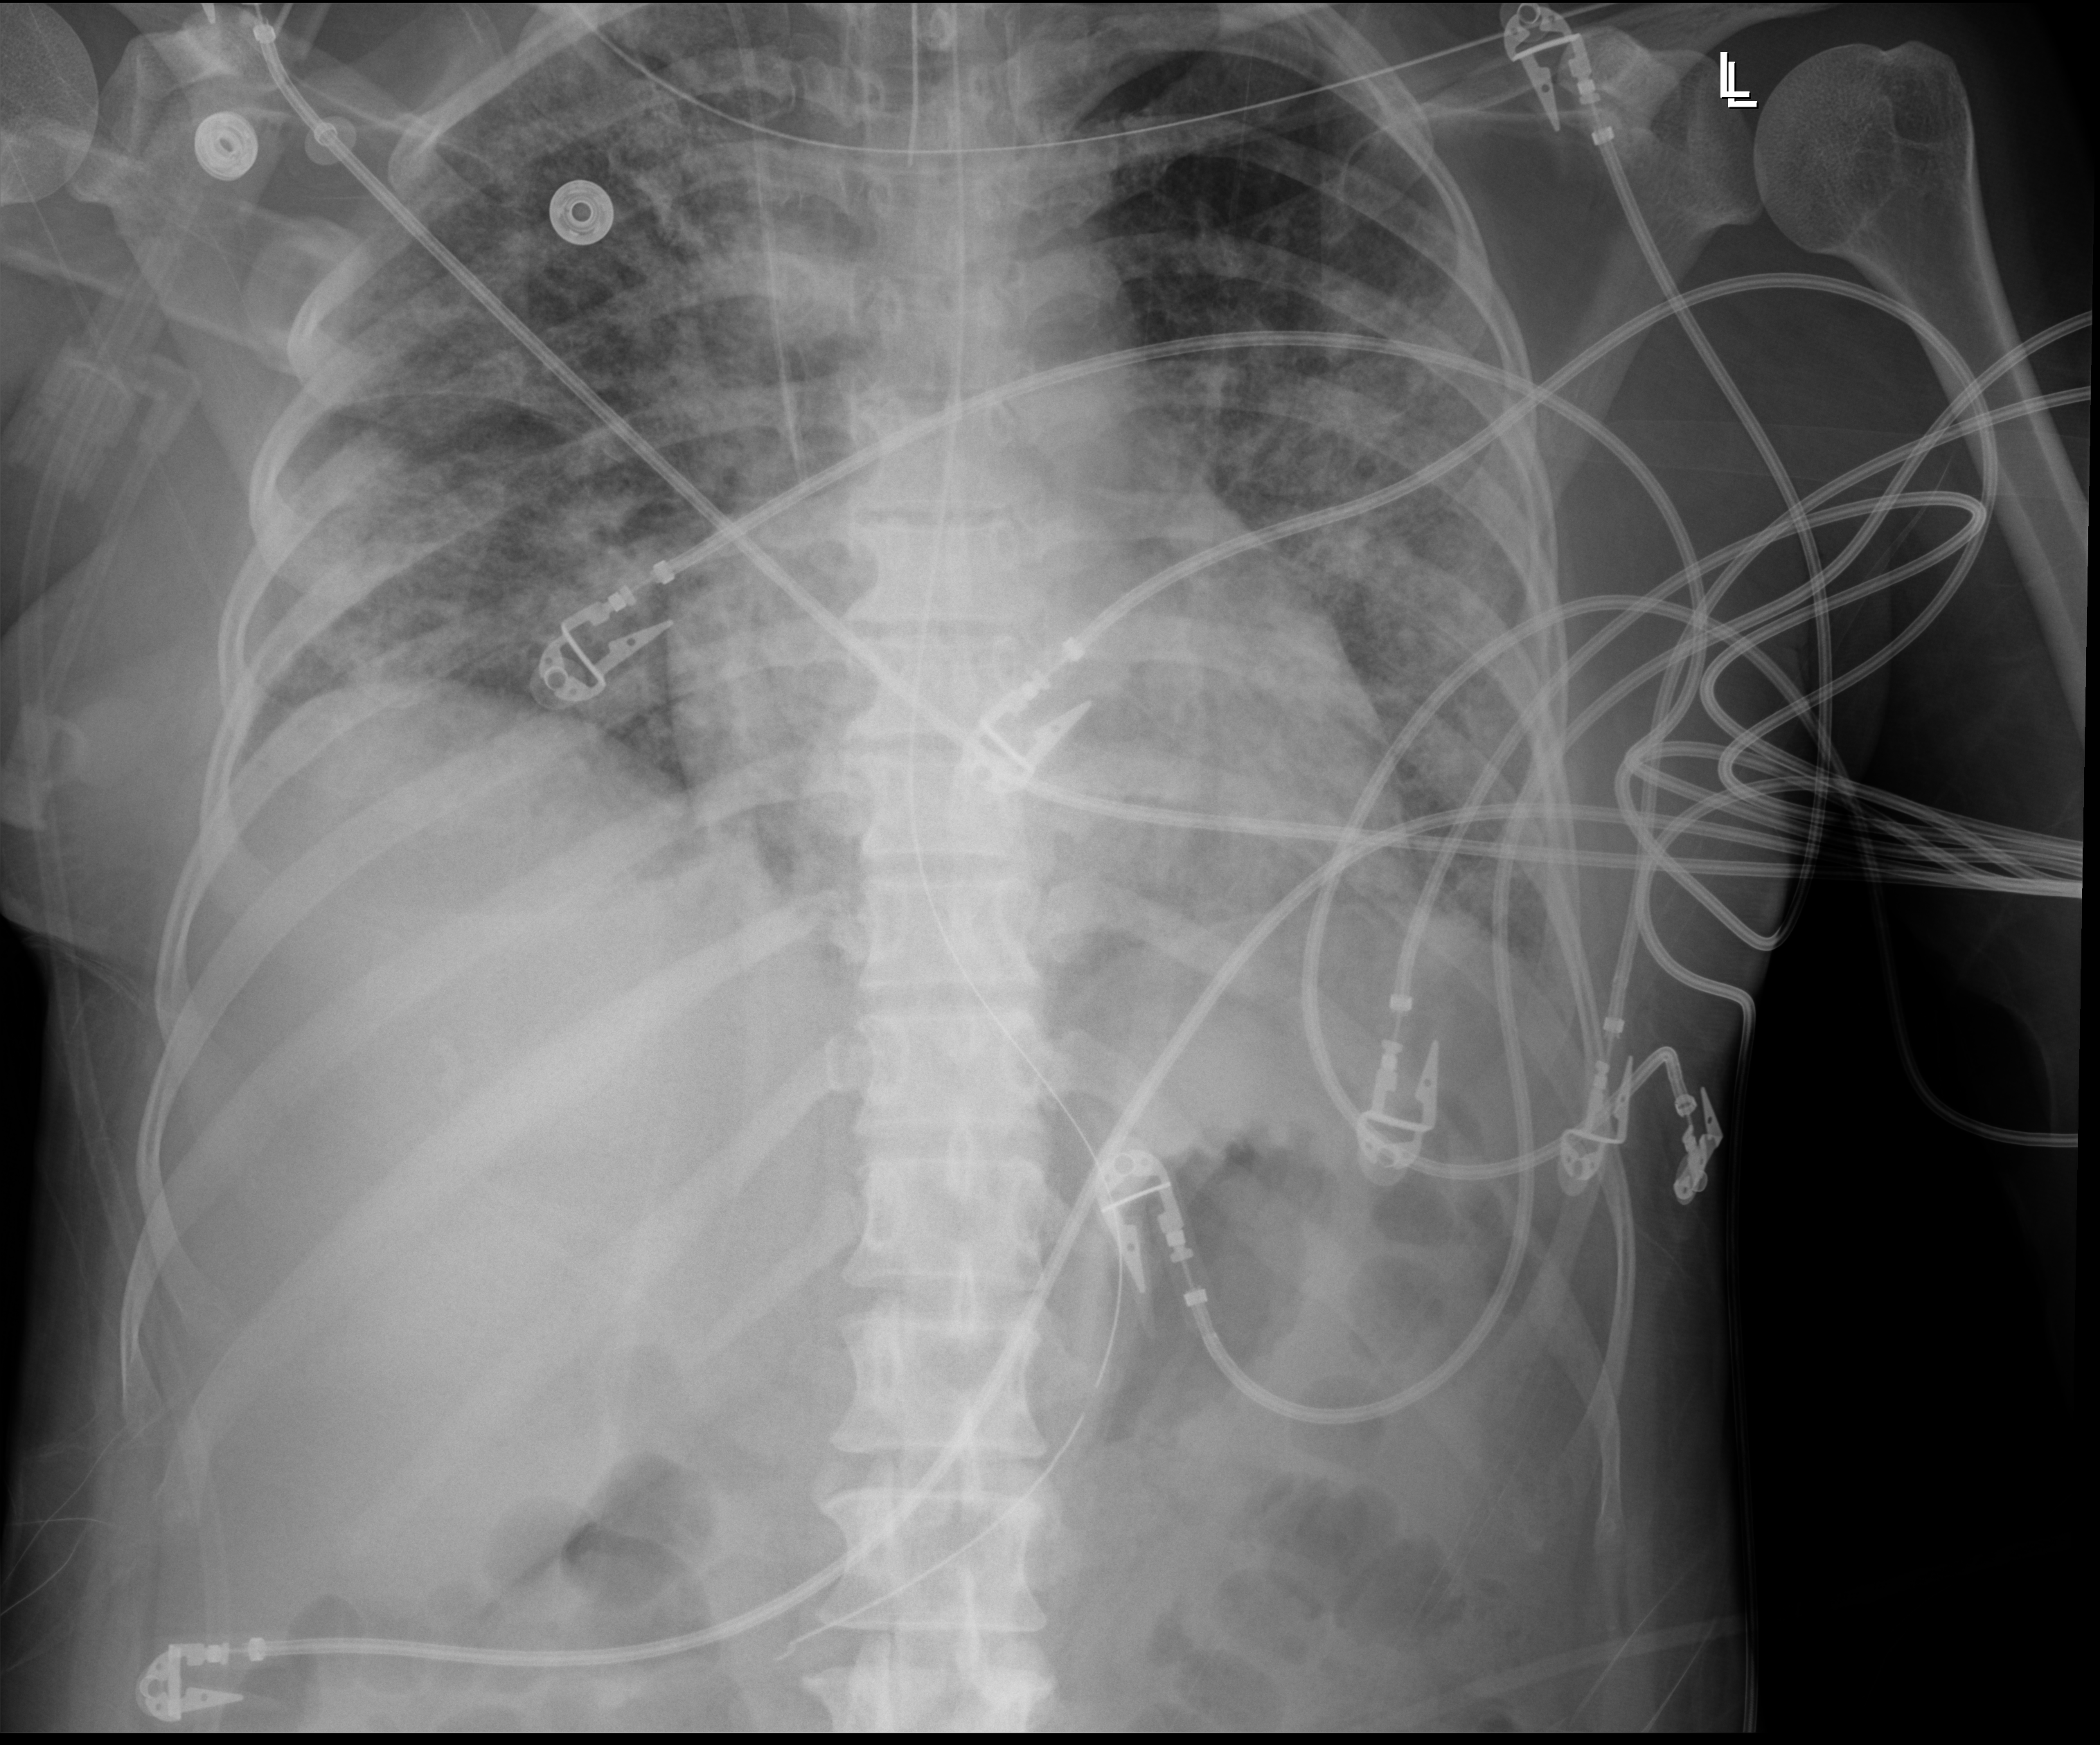
Portable chest radiograph. Female patient hospitalised with COVID-19, age 18–59 years.
Hospital-stay facts (about this admission, not read from this image; timing relative to this image not recorded): admitted to intensive care during this hospital stay: yes; diabetes (admission record): no; mechanically ventilated during this hospital stay: yes.